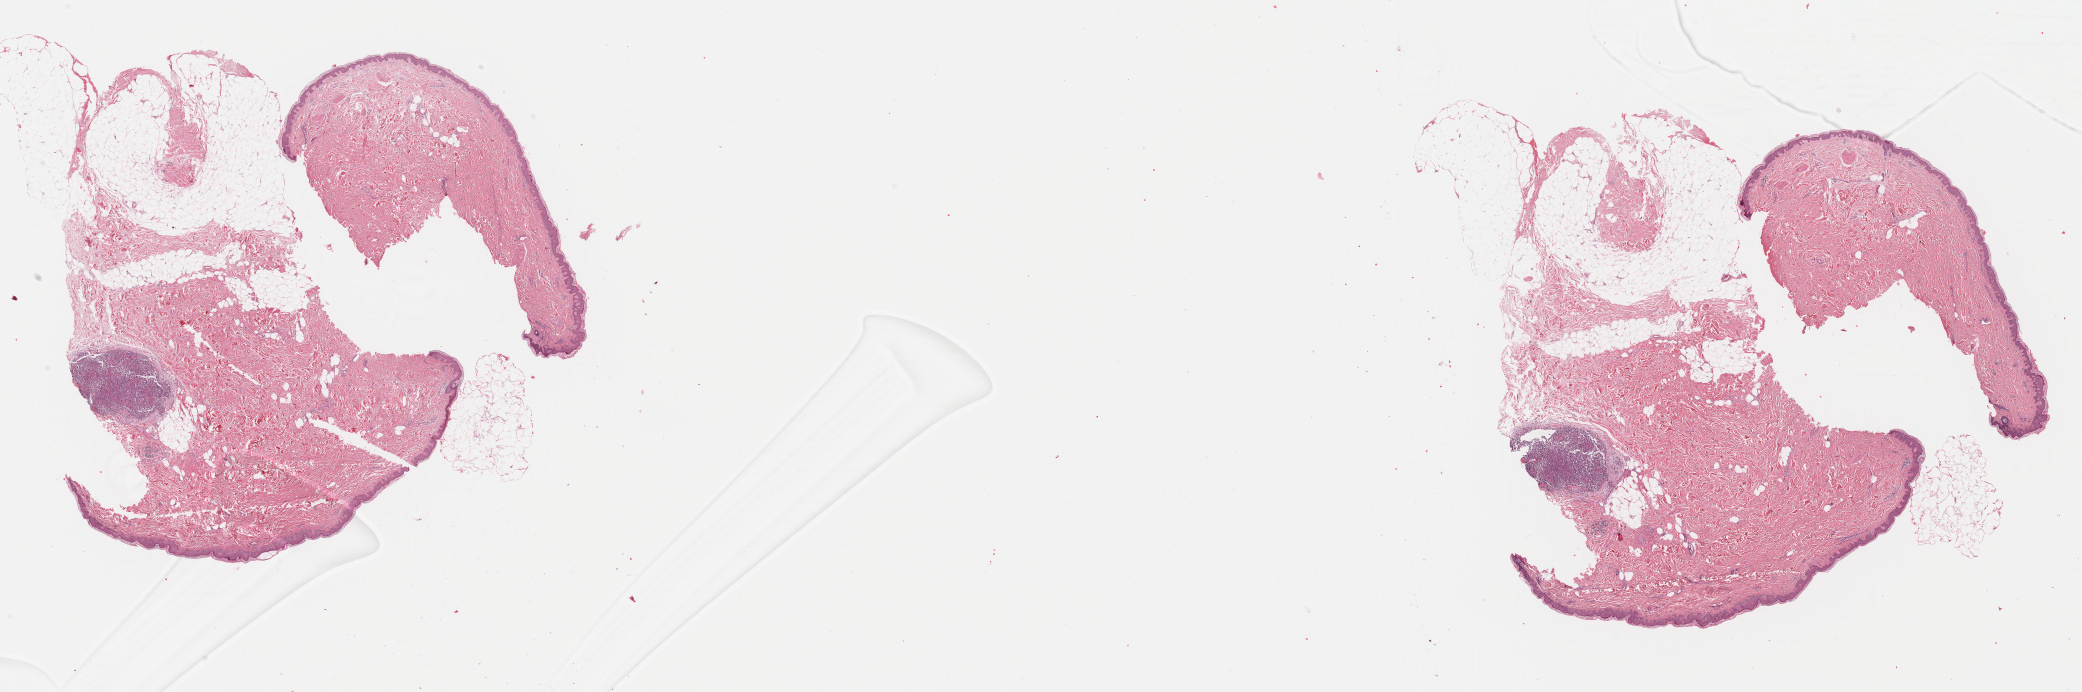
H&E whole-slide image, low-resolution overview of the scanned area, about 32.7 x 10.9 mm (slide scanned at 40x), formalin-fixed paraffin-embedded (FFPE) diagnostic section, metastatic tumour sample, sampled site: skin. Patient: female, age at initial diagnosis 70 years.
This section: metastatic tumour tissue. Patient diagnosis: Malignant melanoma, NOS.